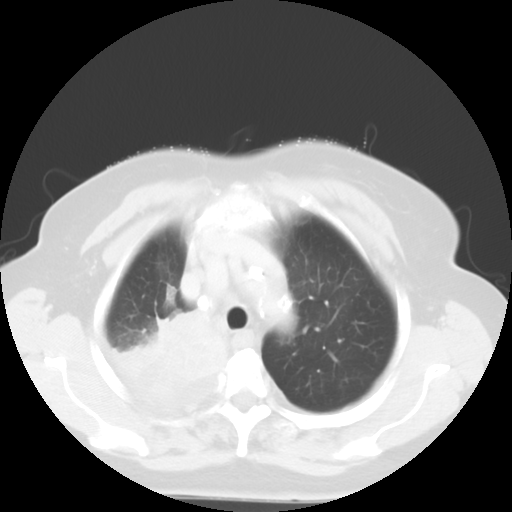
Chest CT, one axial slice; position 43 of 52 along the scan axis; 120 kVp; lung window (W 1500 / L -600 HU); 512 × 512 image matrix. Patient: female, 81 years. From the clinical record (not read from this slice): clinical TNM (as recorded): T4 N3 M1b.
Annotated regions visible in this slice (bounding box drawn by a radiologist):
- lung tumour (recorded histology: adenocarcinoma): bounding box <112,305,230,407> (left, top, right, bottom; pixels)